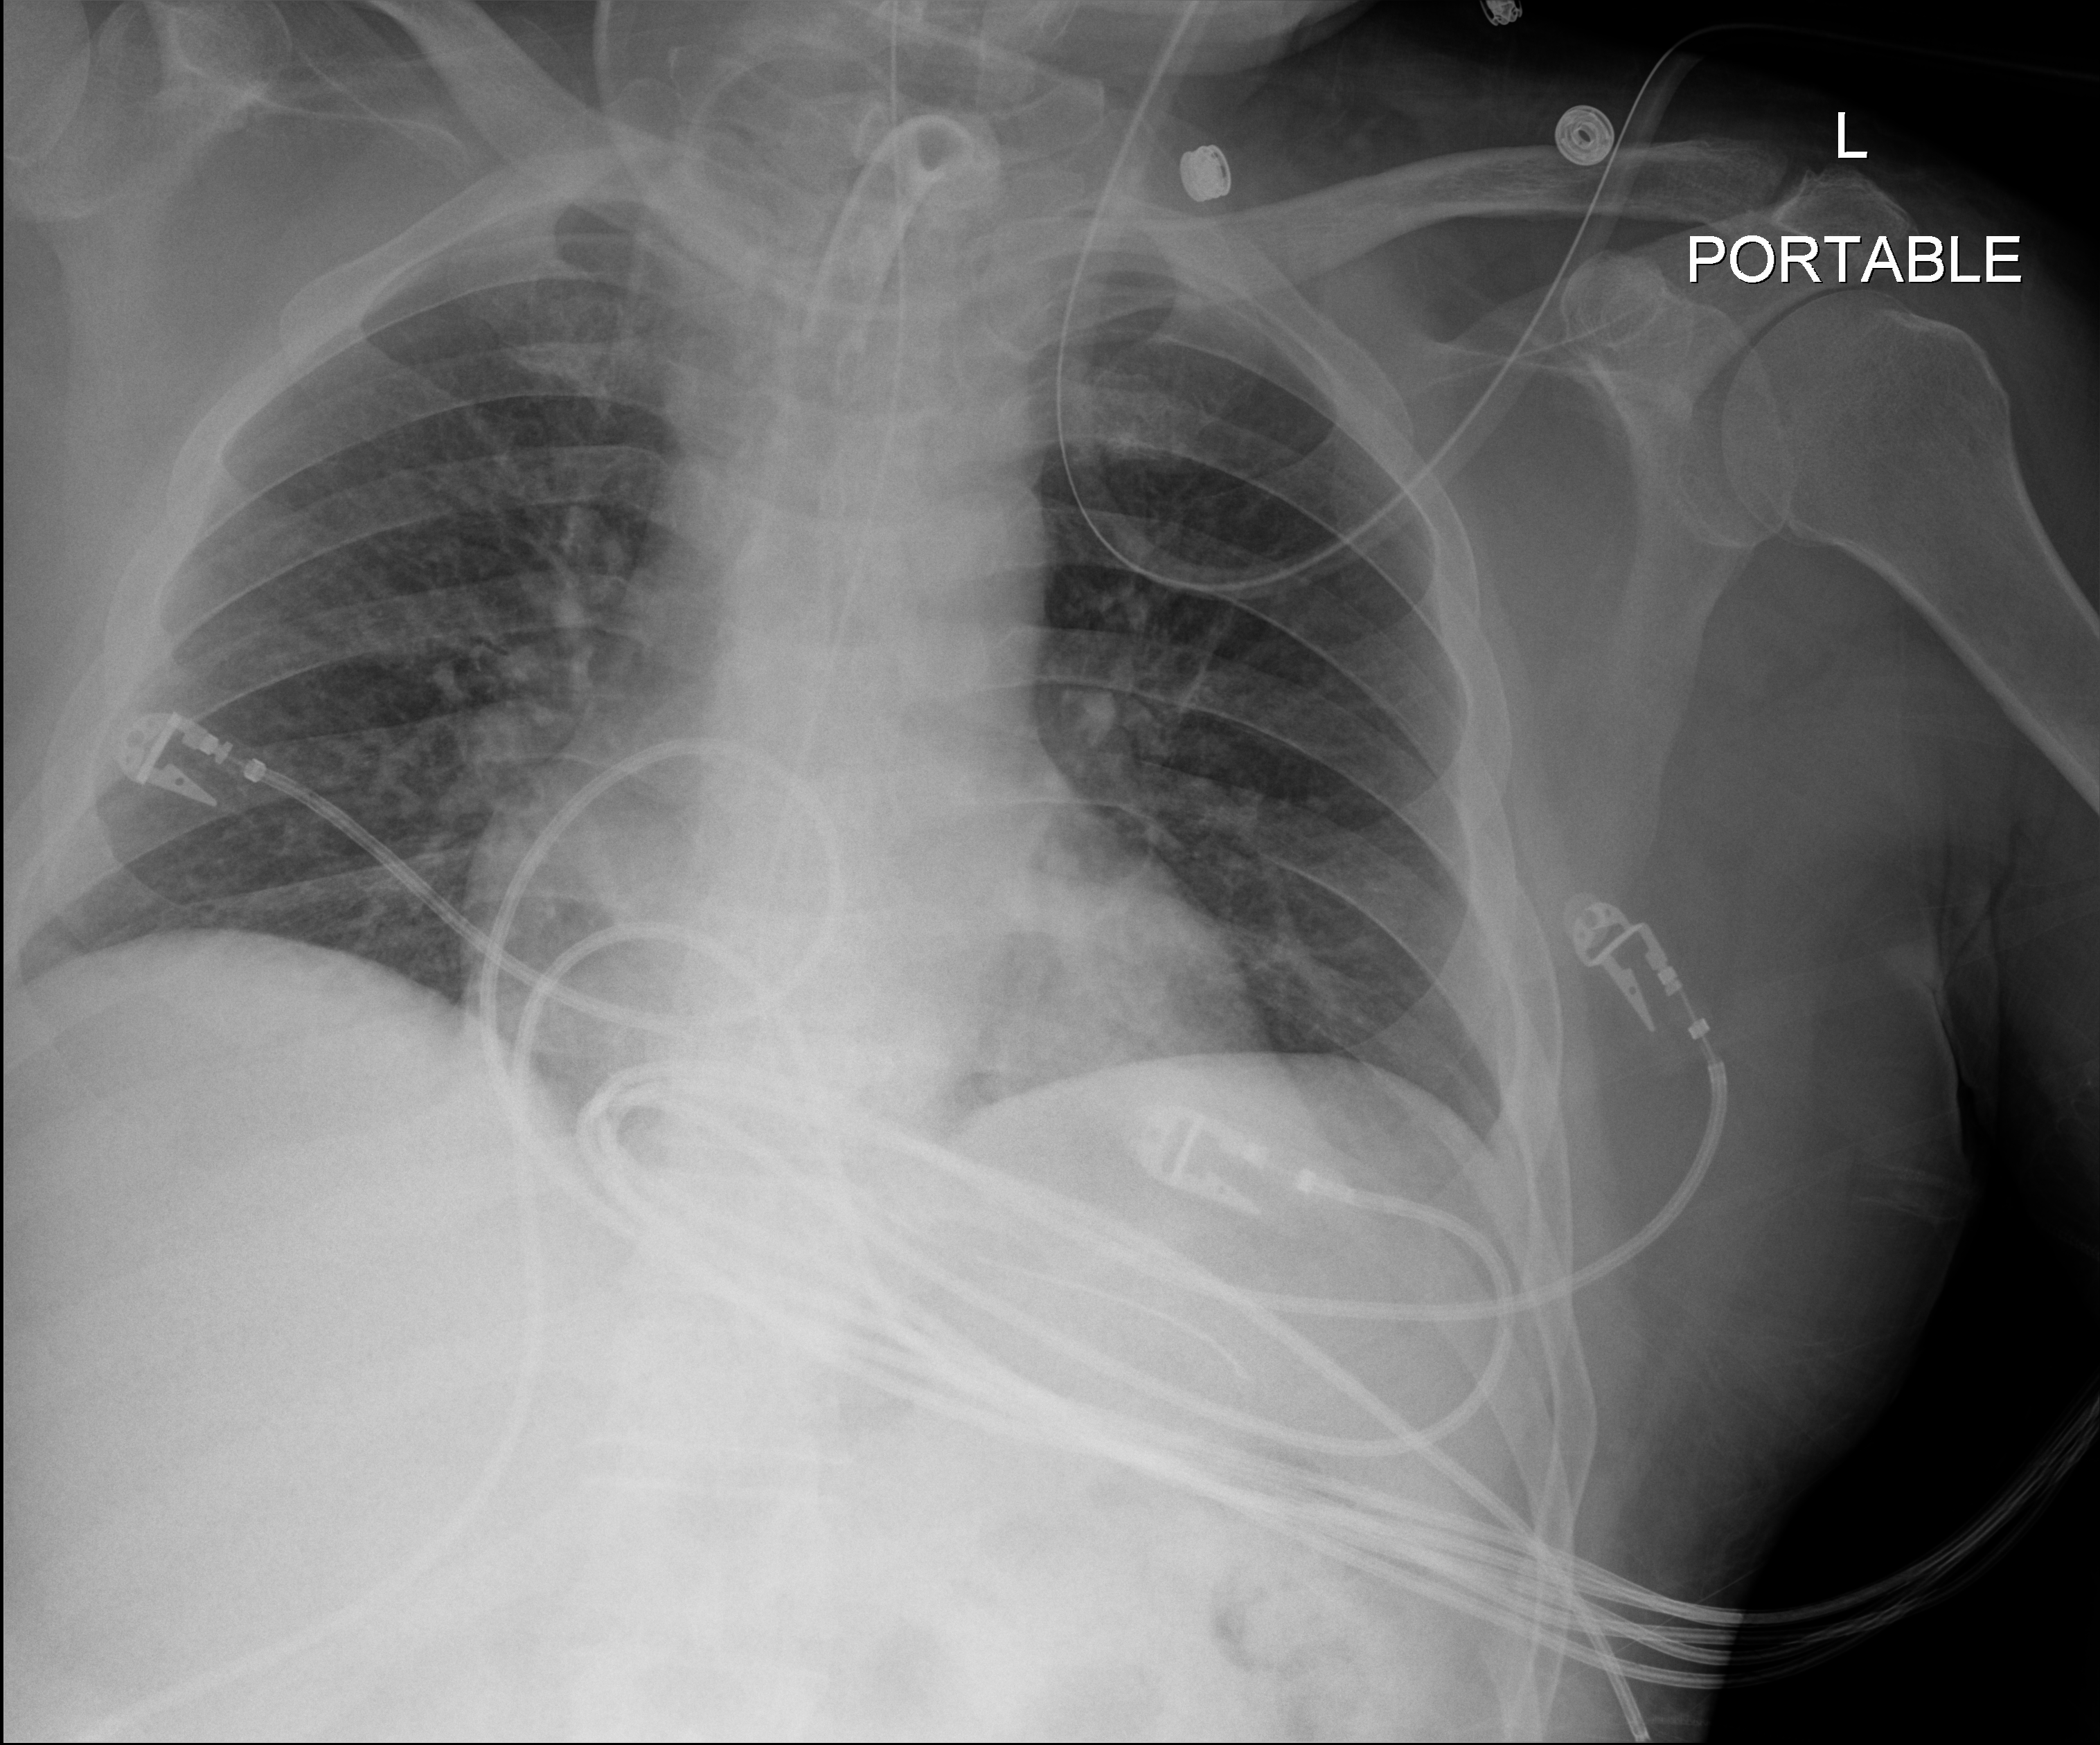
Chest X-ray (portable), anteroposterior (AP) projection. Male patient hospitalised with COVID-19, age 18–59 years.
Admission-level facts for this patient (not findings on this image; timing relative to this image not recorded): length of hospital stay: 65 days; admitted to intensive care during this hospital stay: yes; mechanically ventilated during this hospital stay: yes.